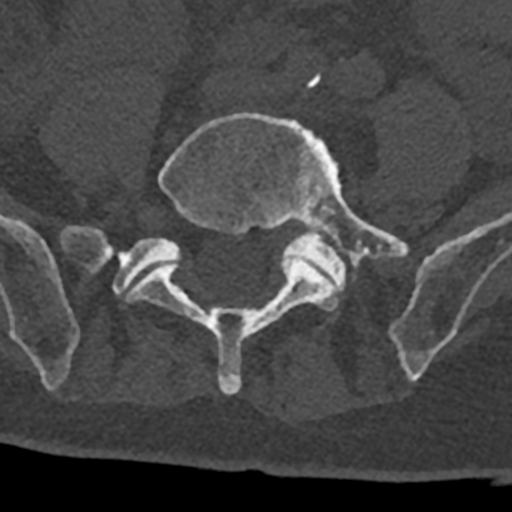
CT including the spine, one axial slice. Position 192 of 797 along the scan axis. Reconstruction kernel Br40s/3. Bone window (W 1800 / L 400 HU). 512 × 512 image matrix, field of view 160 × 160 mm. Male patient, age 74 years. From the clinical record (not read from this slice): primary cancer: renal; vertebrae with lytic lesions (as recorded): T10, L1, L2, L3, L4, L5.
Outlined on this slice (semi-automatically segmented with operator editing):
- L5 vertebra: box from (x=126, y=113) to (x=409, y=394) px